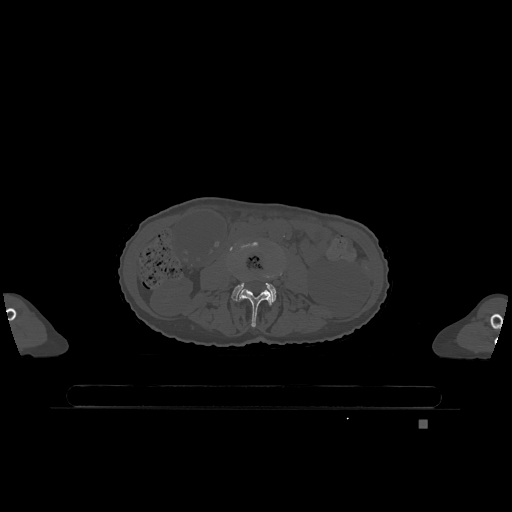
CT including the spine, one axial slice; position 338 of 1317 along the scan axis; bone window (W 1800 / L 400 HU); 0.5 mm slice thickness; 512 × 512 image matrix, field of view 500 × 500 mm. Patient: female, 74 years. From the clinical record (not read from this slice): primary cancer: lung; vertebrae with lytic lesions (as recorded): T1, T4, T5, T6, L4, L5.
Structures marked on this image (semi-automatic segmentation, software-assisted and operator-edited):
- L3 vertebra: bounding box (x1, y1, x2, y2) in pixels: (238, 270, 283, 327)
- L4 vertebra: (230, 246, 277, 302)